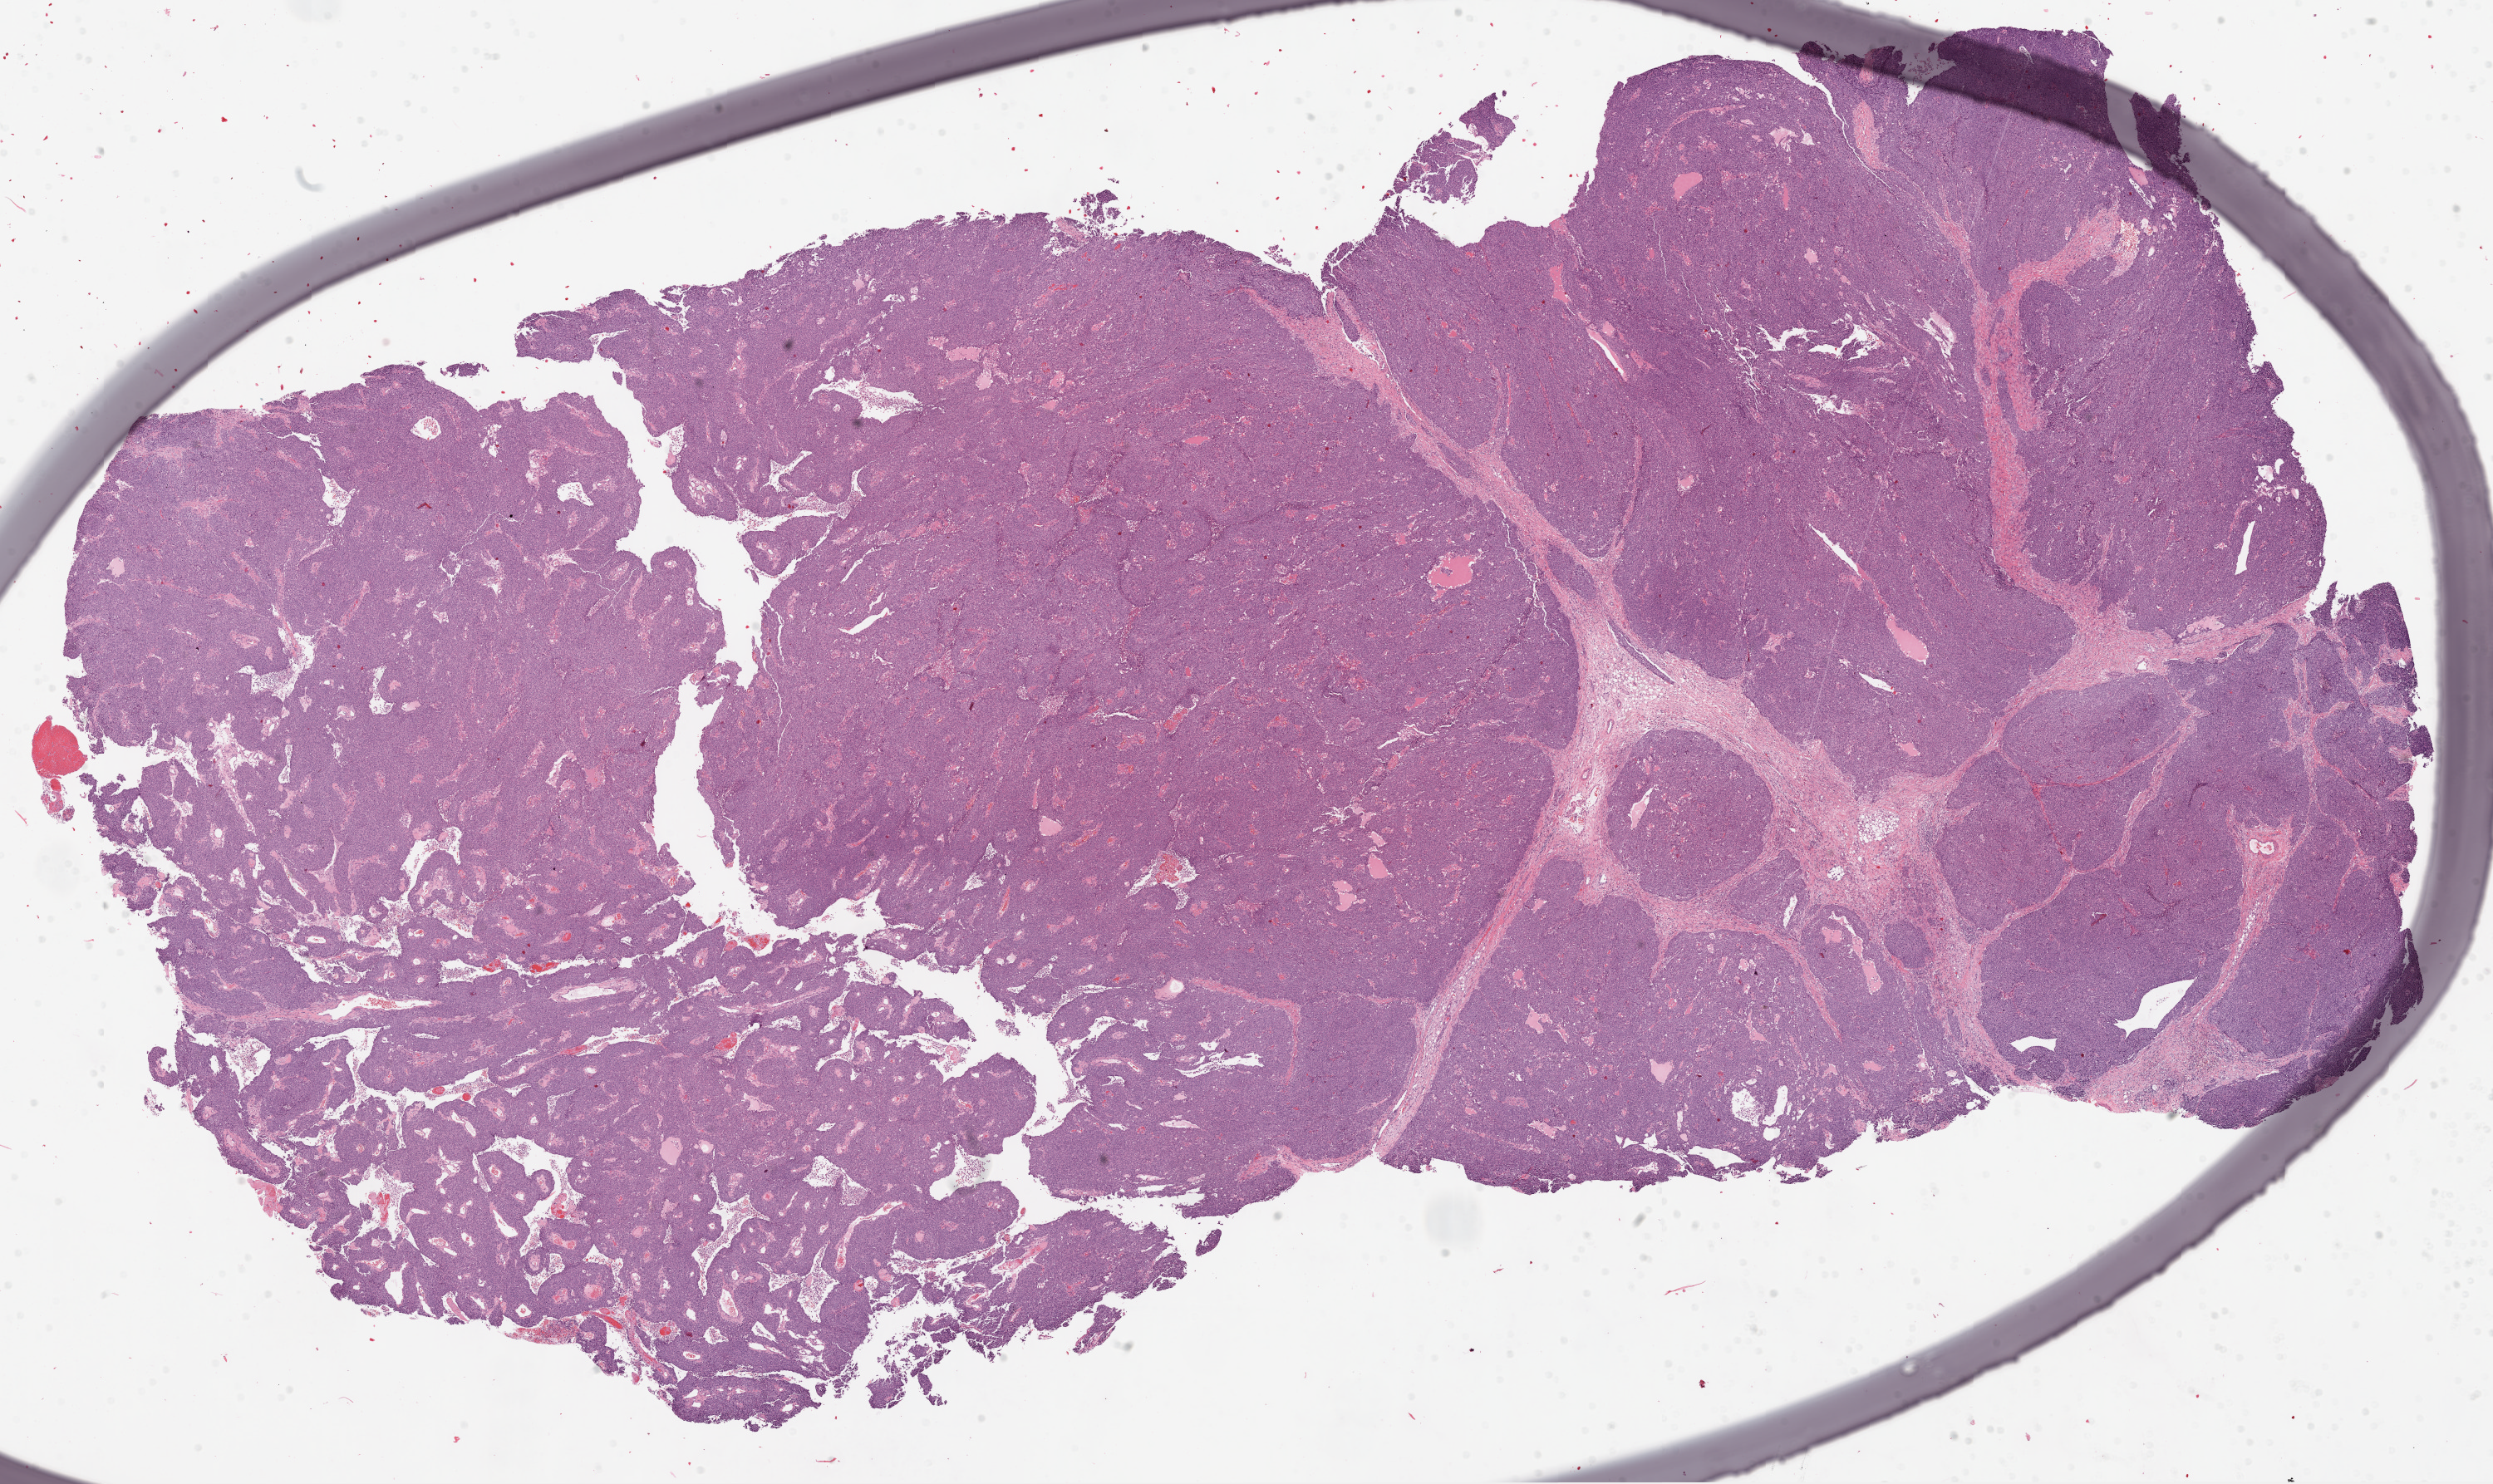
Whole-slide histology image, Hematoxylin and eosin (H&E) stained, a low-resolution overview of the entire scanned area, about 24.1 x 14.3 mm (slide scanned at 20x), frozen section, primary tumour sample from the ovary. Female patient; age at initial diagnosis 38 years. Histologic grade: G3 (poorly differentiated). Pathologist review of this section (percent, as recorded): tumour cells 88%, tumour nuclei 85%, normal cells 0%, stromal cells 7%, necrosis 5%.
Histologic diagnosis: Serous cystadenocarcinoma, NOS. FIGO stage: IIIC.